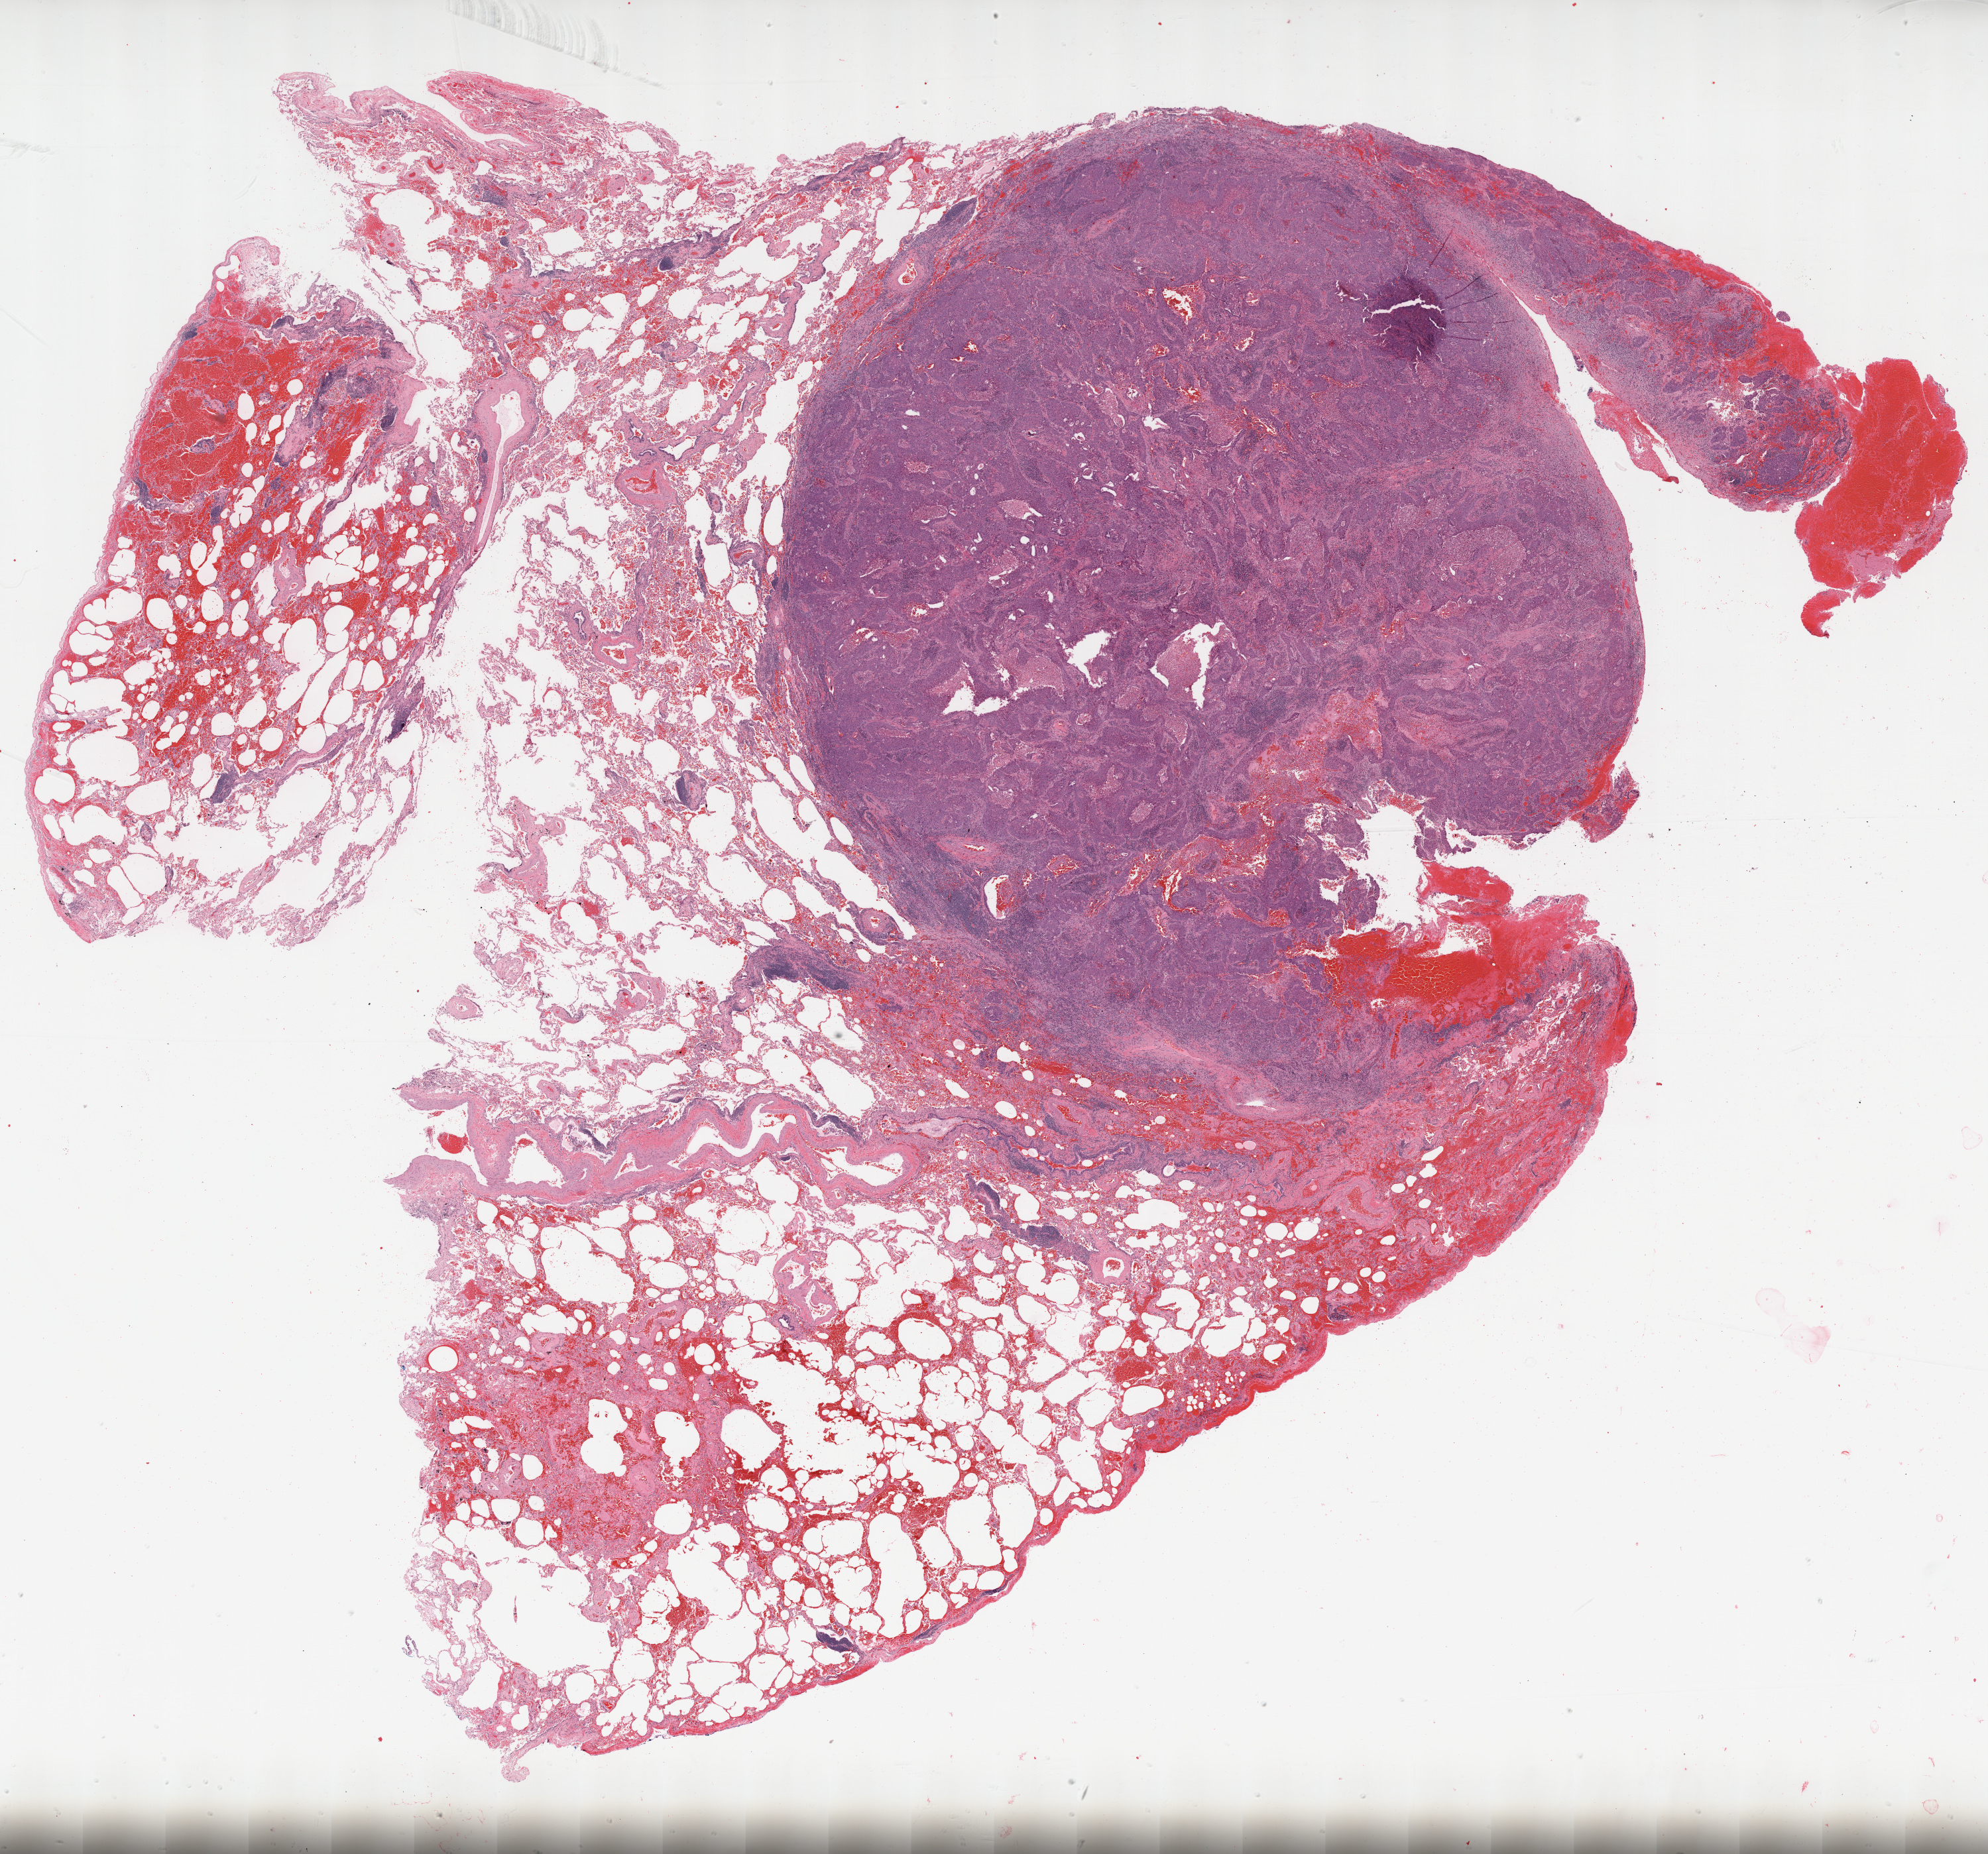
Hematoxylin and eosin (H&E) stained whole-slide image, low-resolution overview of the scanned area, about 24.1 x 22.5 mm, formalin-fixed paraffin-embedded (FFPE) diagnostic section, primary tumour sample from the lung. Female patient; age at initial diagnosis 74 years.
Diagnosis: Squamous cell carcinoma, NOS. TNM: T2 N0 M0. AJCC pathologic stage: IB.